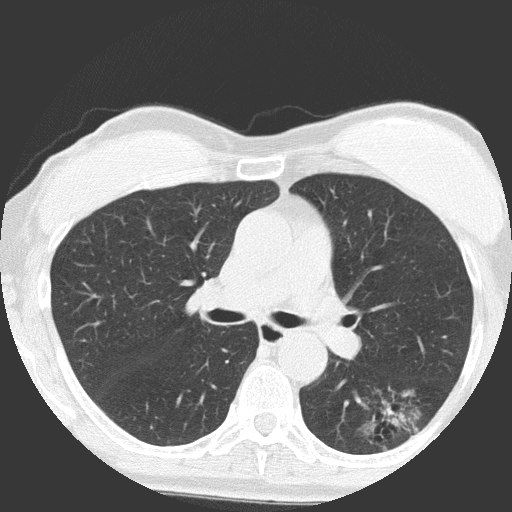
Low-dose screening chest CT, axial slice. First (baseline) screen. Lung window (W 1500 / L -600 HU). Slice 58 of 149 in the series. 512 × 512 image matrix, field of view 300 × 300 mm. Female, age 64 years at enrolment. Former smoker at enrolment.
Expert-annotated lung lesion, bounding box (x1, y1, x2, y2) in pixels: (344, 386, 430, 459). Reader record for this screening exam (exam-level; its link to the box is not recorded): non-calcified nodule or mass ≥4 mm, right upper lobe, 4 × 4 mm, poorly defined margins, ground glass attenuation. Note: the box lies in the patient's left hemithorax on this image, whereas the reader's record names the right lung; they may be different findings. Official screen result: positive, change unspecified: nodule(s) >= 4 mm or enlarging nodule(s), mass(es), or other non-specific abnormalities suspicious for lung cancer. Lung cancer was diagnosed 932 days after this screen: adenocarcinoma, NOS, left lower lobe, moderately differentiated (G2), stage IA (AJCC 6th edition), 17 mm at pathology.